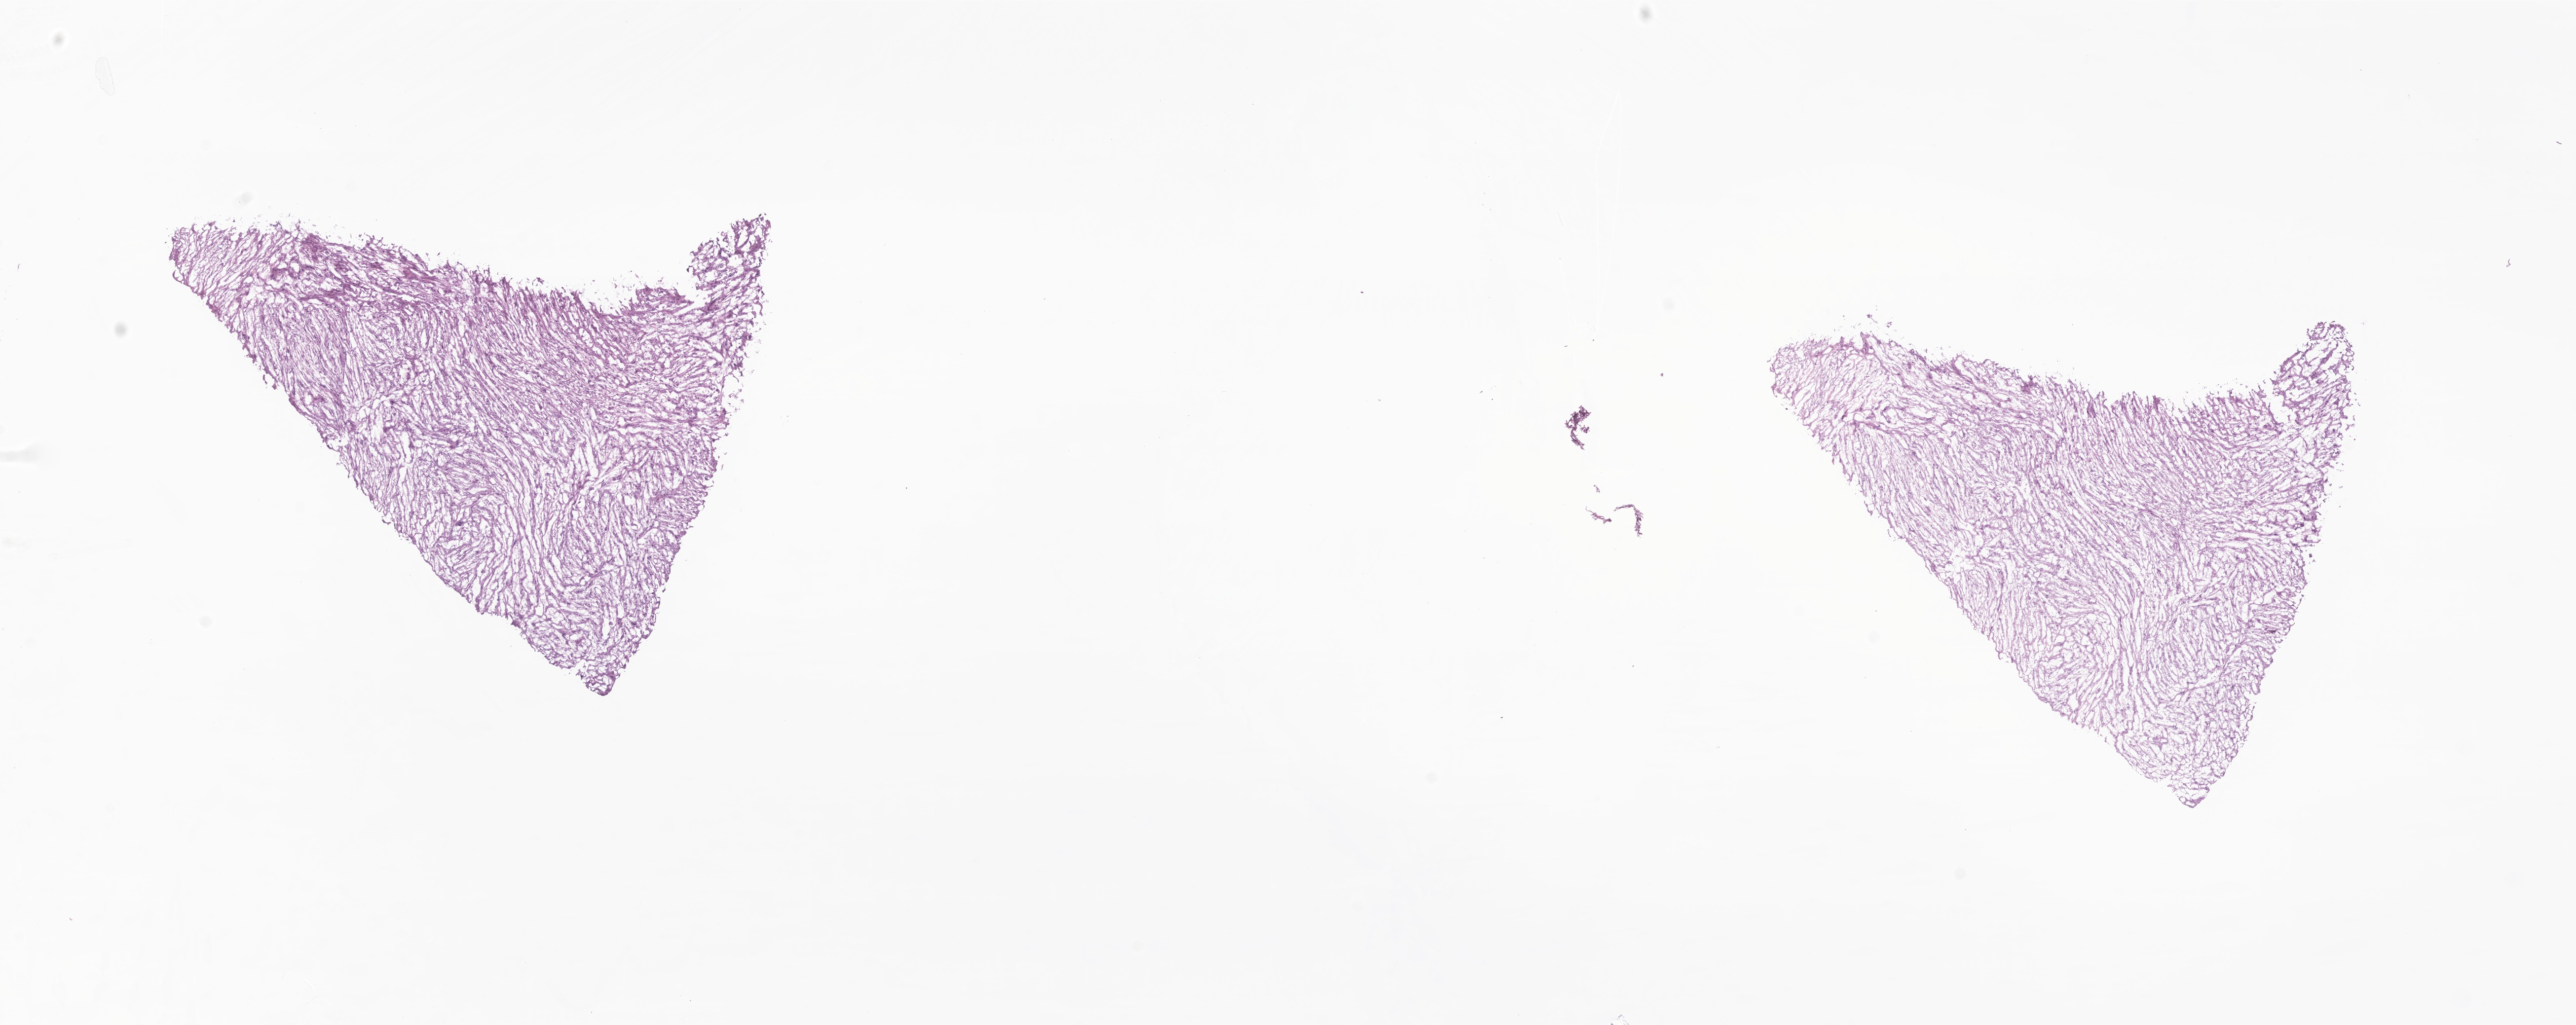
H&E whole-slide image of tumor tissue from the brain — low-resolution overview of the scanned area, about 22.0 x 8.8 mm. Cryosection (OCT / tissue freezing medium). Patient: female, age 57 months (4 years 9 months).
Diagnosis: Neoplasm, benign.